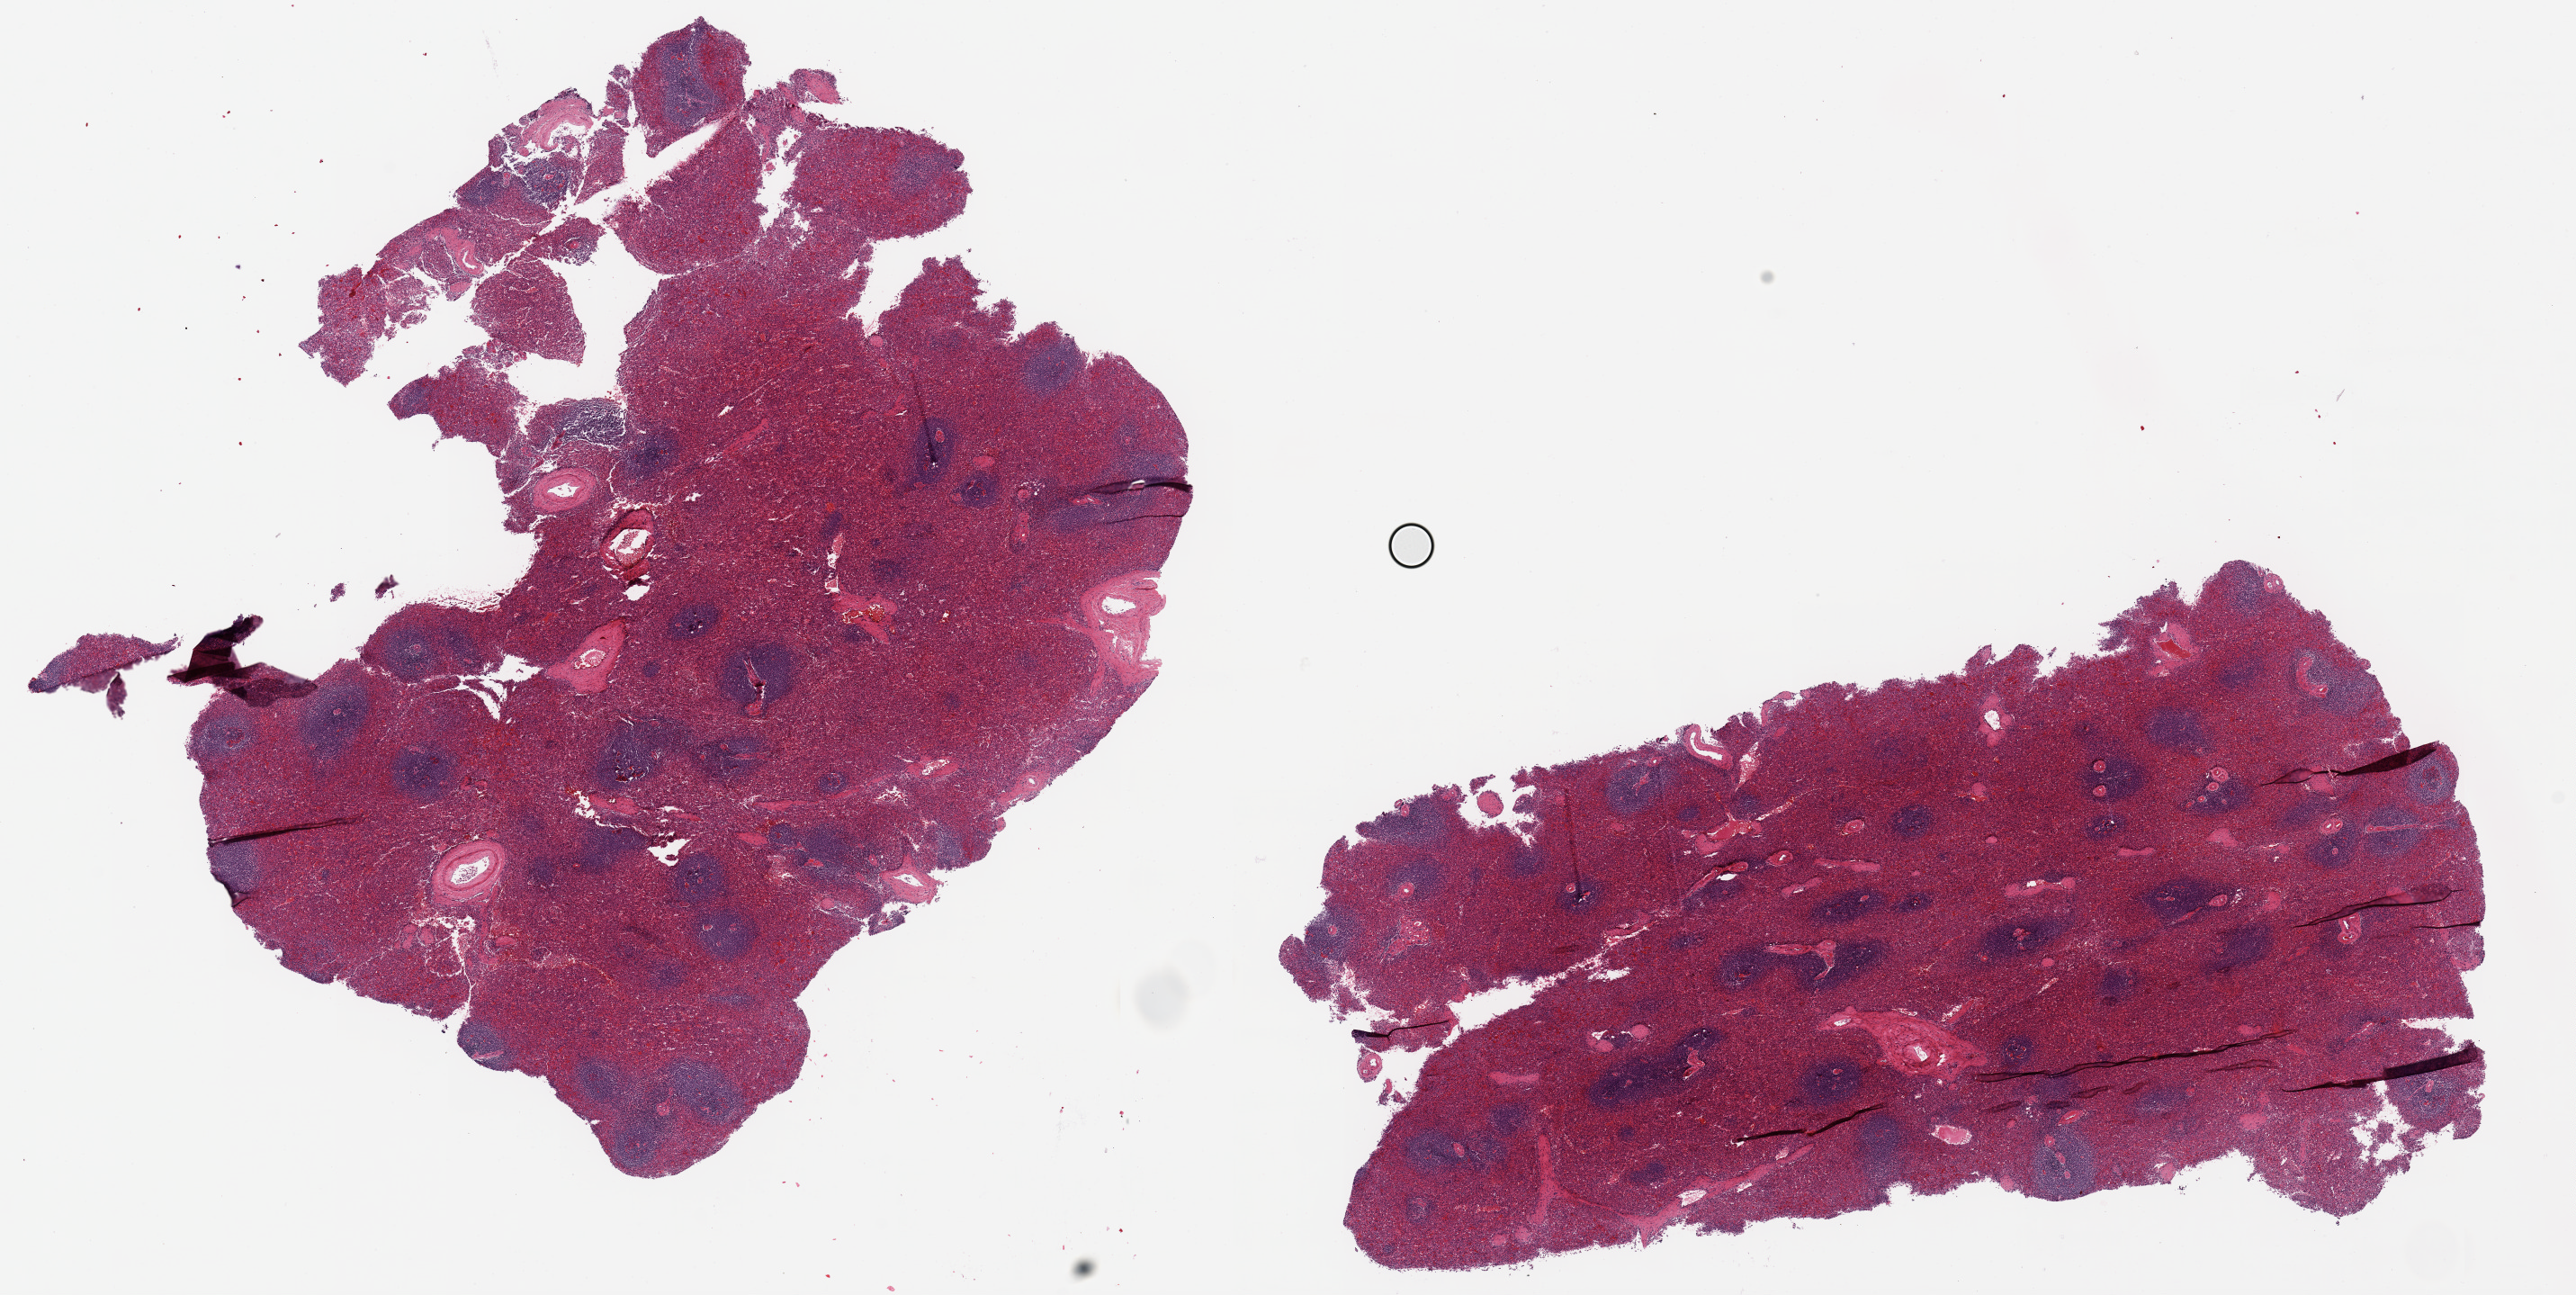
H&E whole-slide image, shown as a low-resolution overview of the whole scanned area (about 22.6 x 11.4 mm, from a 20x scan), PAXgene-fixed, paraffin-embedded tissue, sampled site (target tissue): spleen, tissue donor sample. Donor: male.
Reviewer comment on this tissue sample: 2 pieces ~9x6; well preserved.